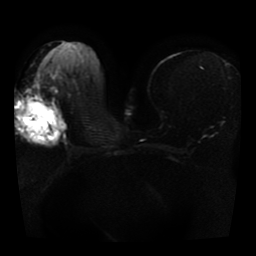
Breast MRI, one axial slice. Position 20 of 41 along the scan axis. Diffusion-weighted series; image 2 of 4 stored at this slice position (different b-values; order by instance number). 1.5 T. 5 mm slice thickness. 256 × 256 image matrix, field of view 330 × 330 mm. Female patient.
Outlined on this slice (outlined manually by an expert reader):
- tumour on diffusion-weighted imaging: bounding box (x1, y1, x2, y2) in pixels: (16, 97, 68, 143)